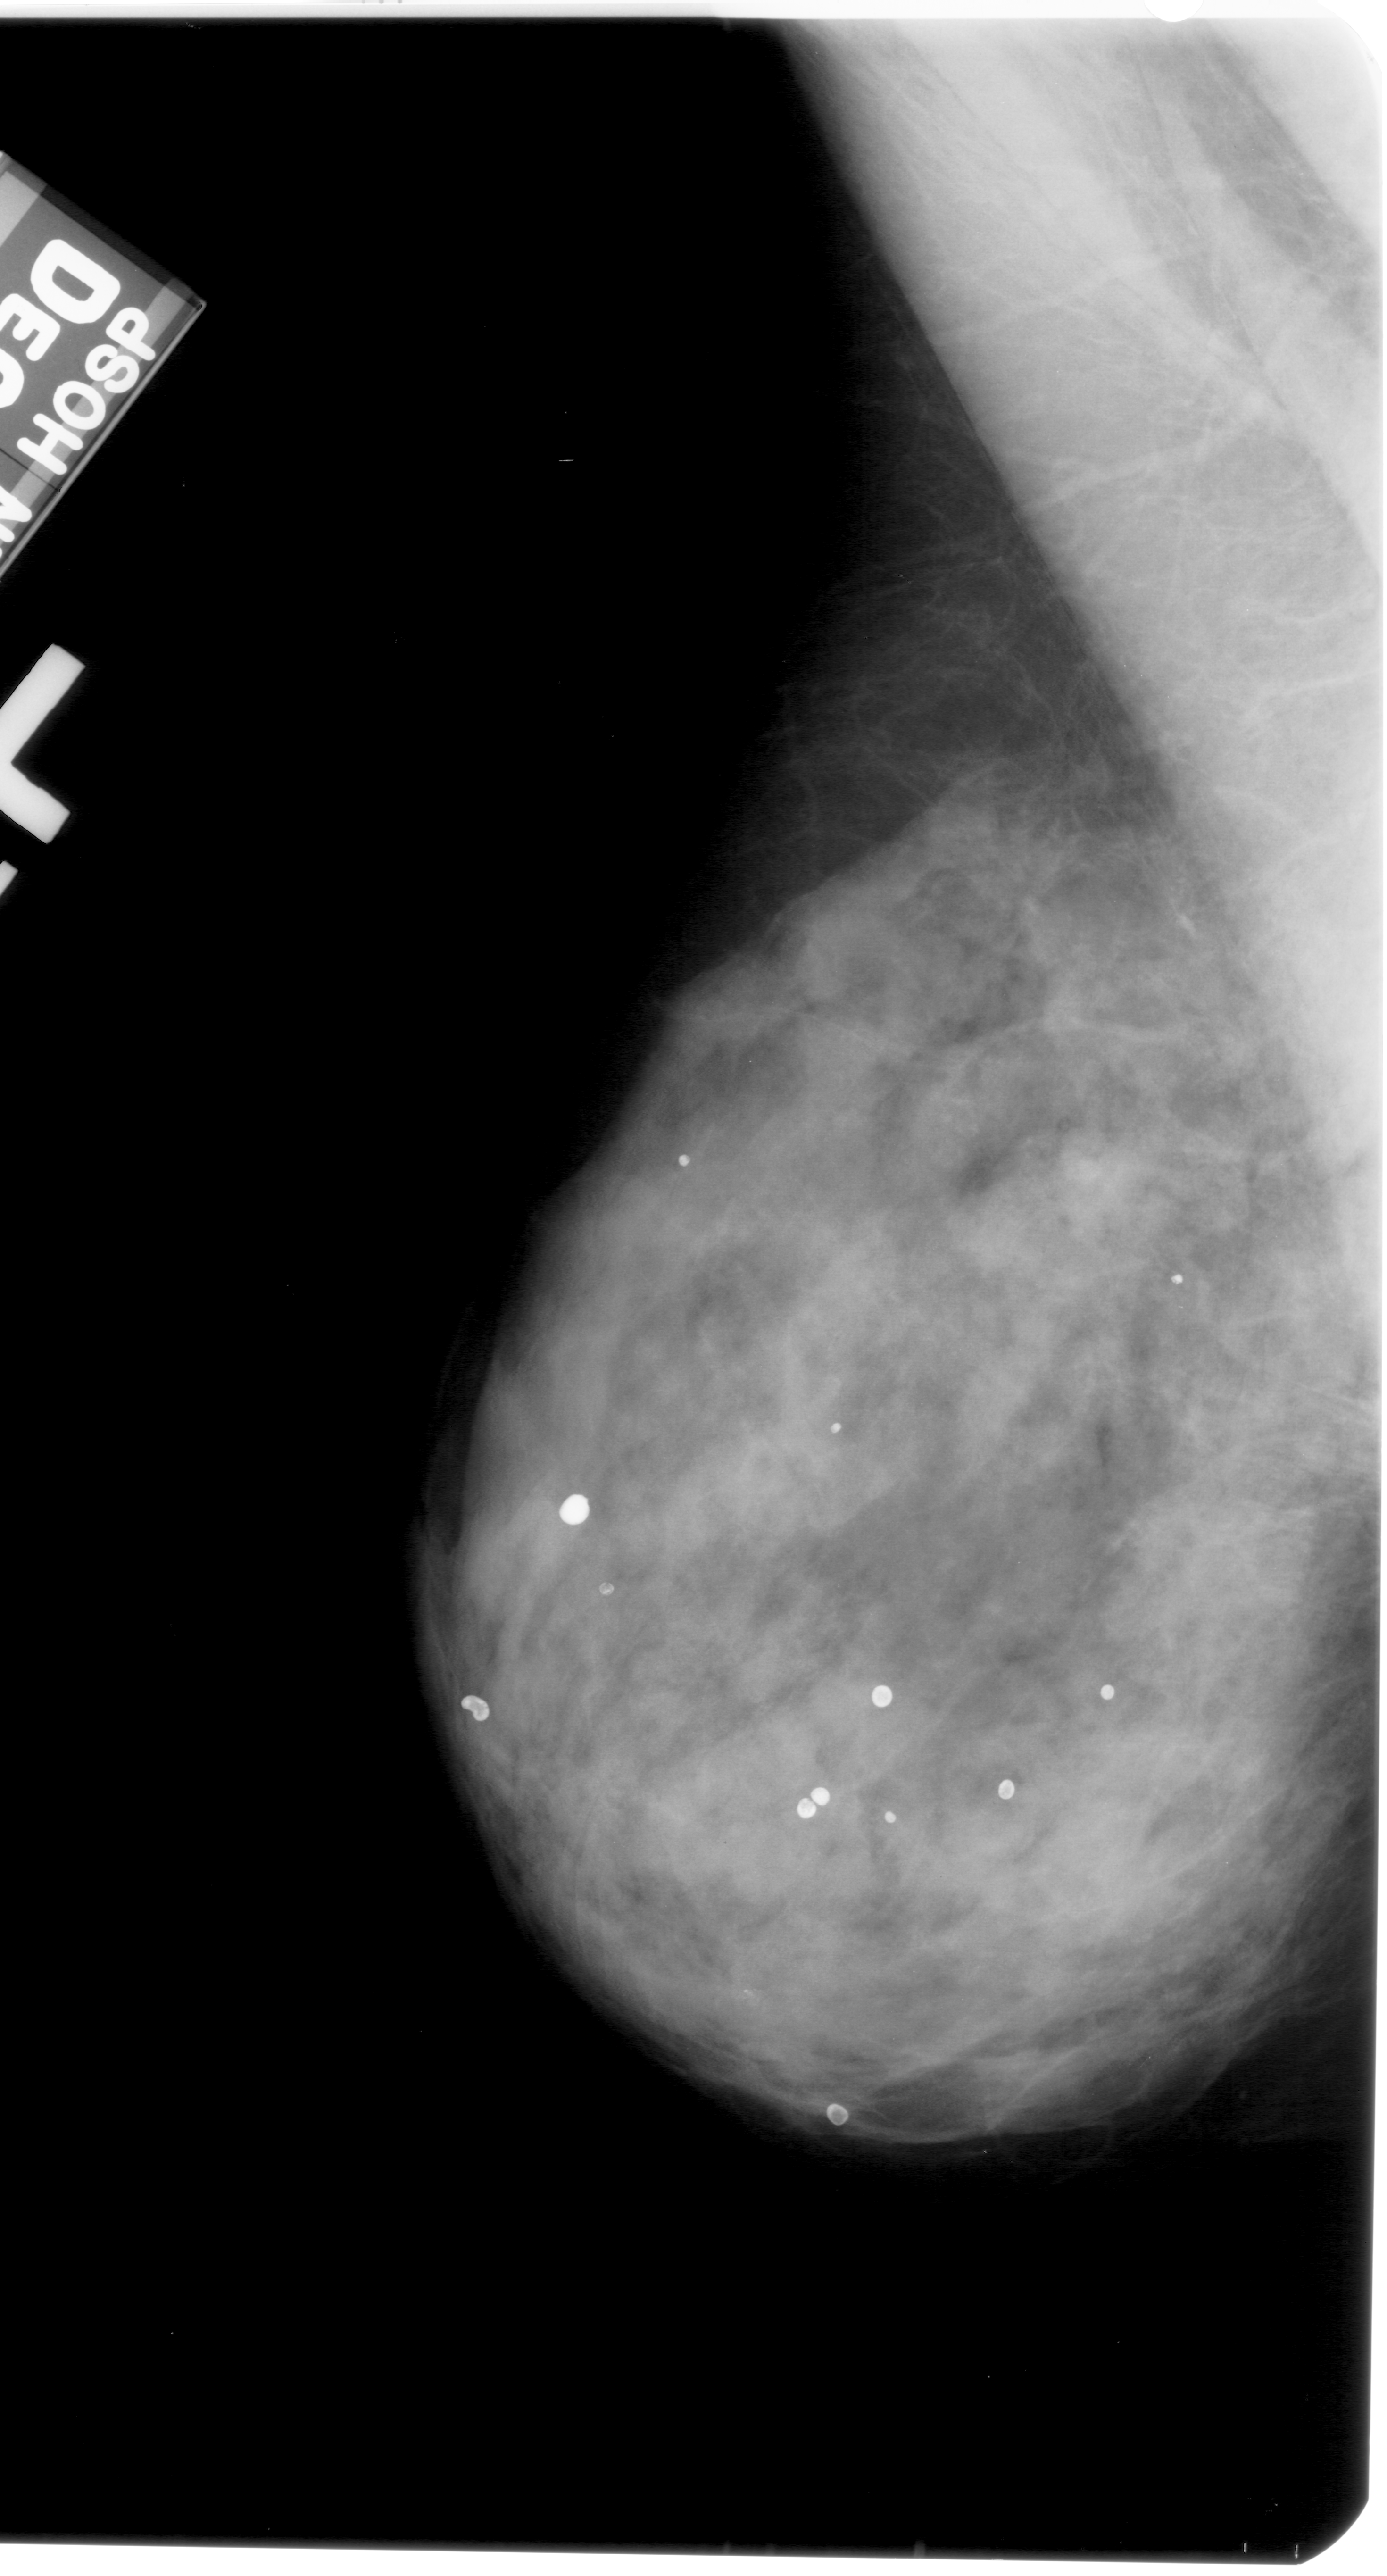
Scanned film-screen mammogram; left breast; mediolateral oblique (MLO) view.
Calcifications, morphology amorphous, distribution clustered; BI-RADS assessment category 4; pathology result (as recorded, not read from the image): benign.